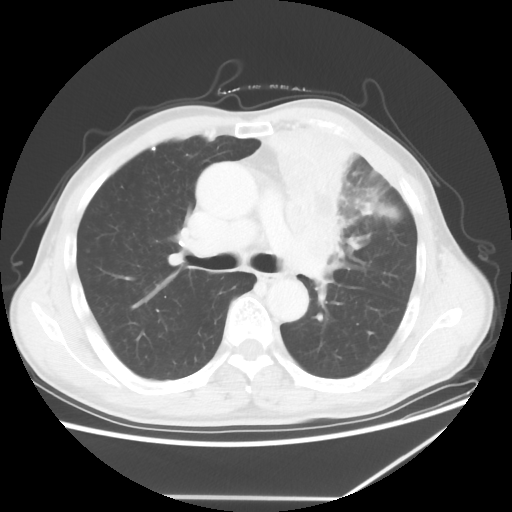
Chest CT, one axial slice; position 39 of 64 along the scan axis; reconstruction kernel STANDARD; 100 kVp; lung window (W 1500 / L -600 HU); 5 mm slice thickness; 512 × 512 image matrix, field of view 383 × 383 mm. Male patient, age 64 years. From the clinical record (not read from this slice): clinical TNM (as recorded): T1c N1 M1; histopathological grade: G2.
Outlined on this slice (rectangle marked by the reading radiologist):
- lung tumour (recorded histology: squamous cell carcinoma): bounding box (x1, y1, x2, y2) in pixels: (251, 119, 369, 276)